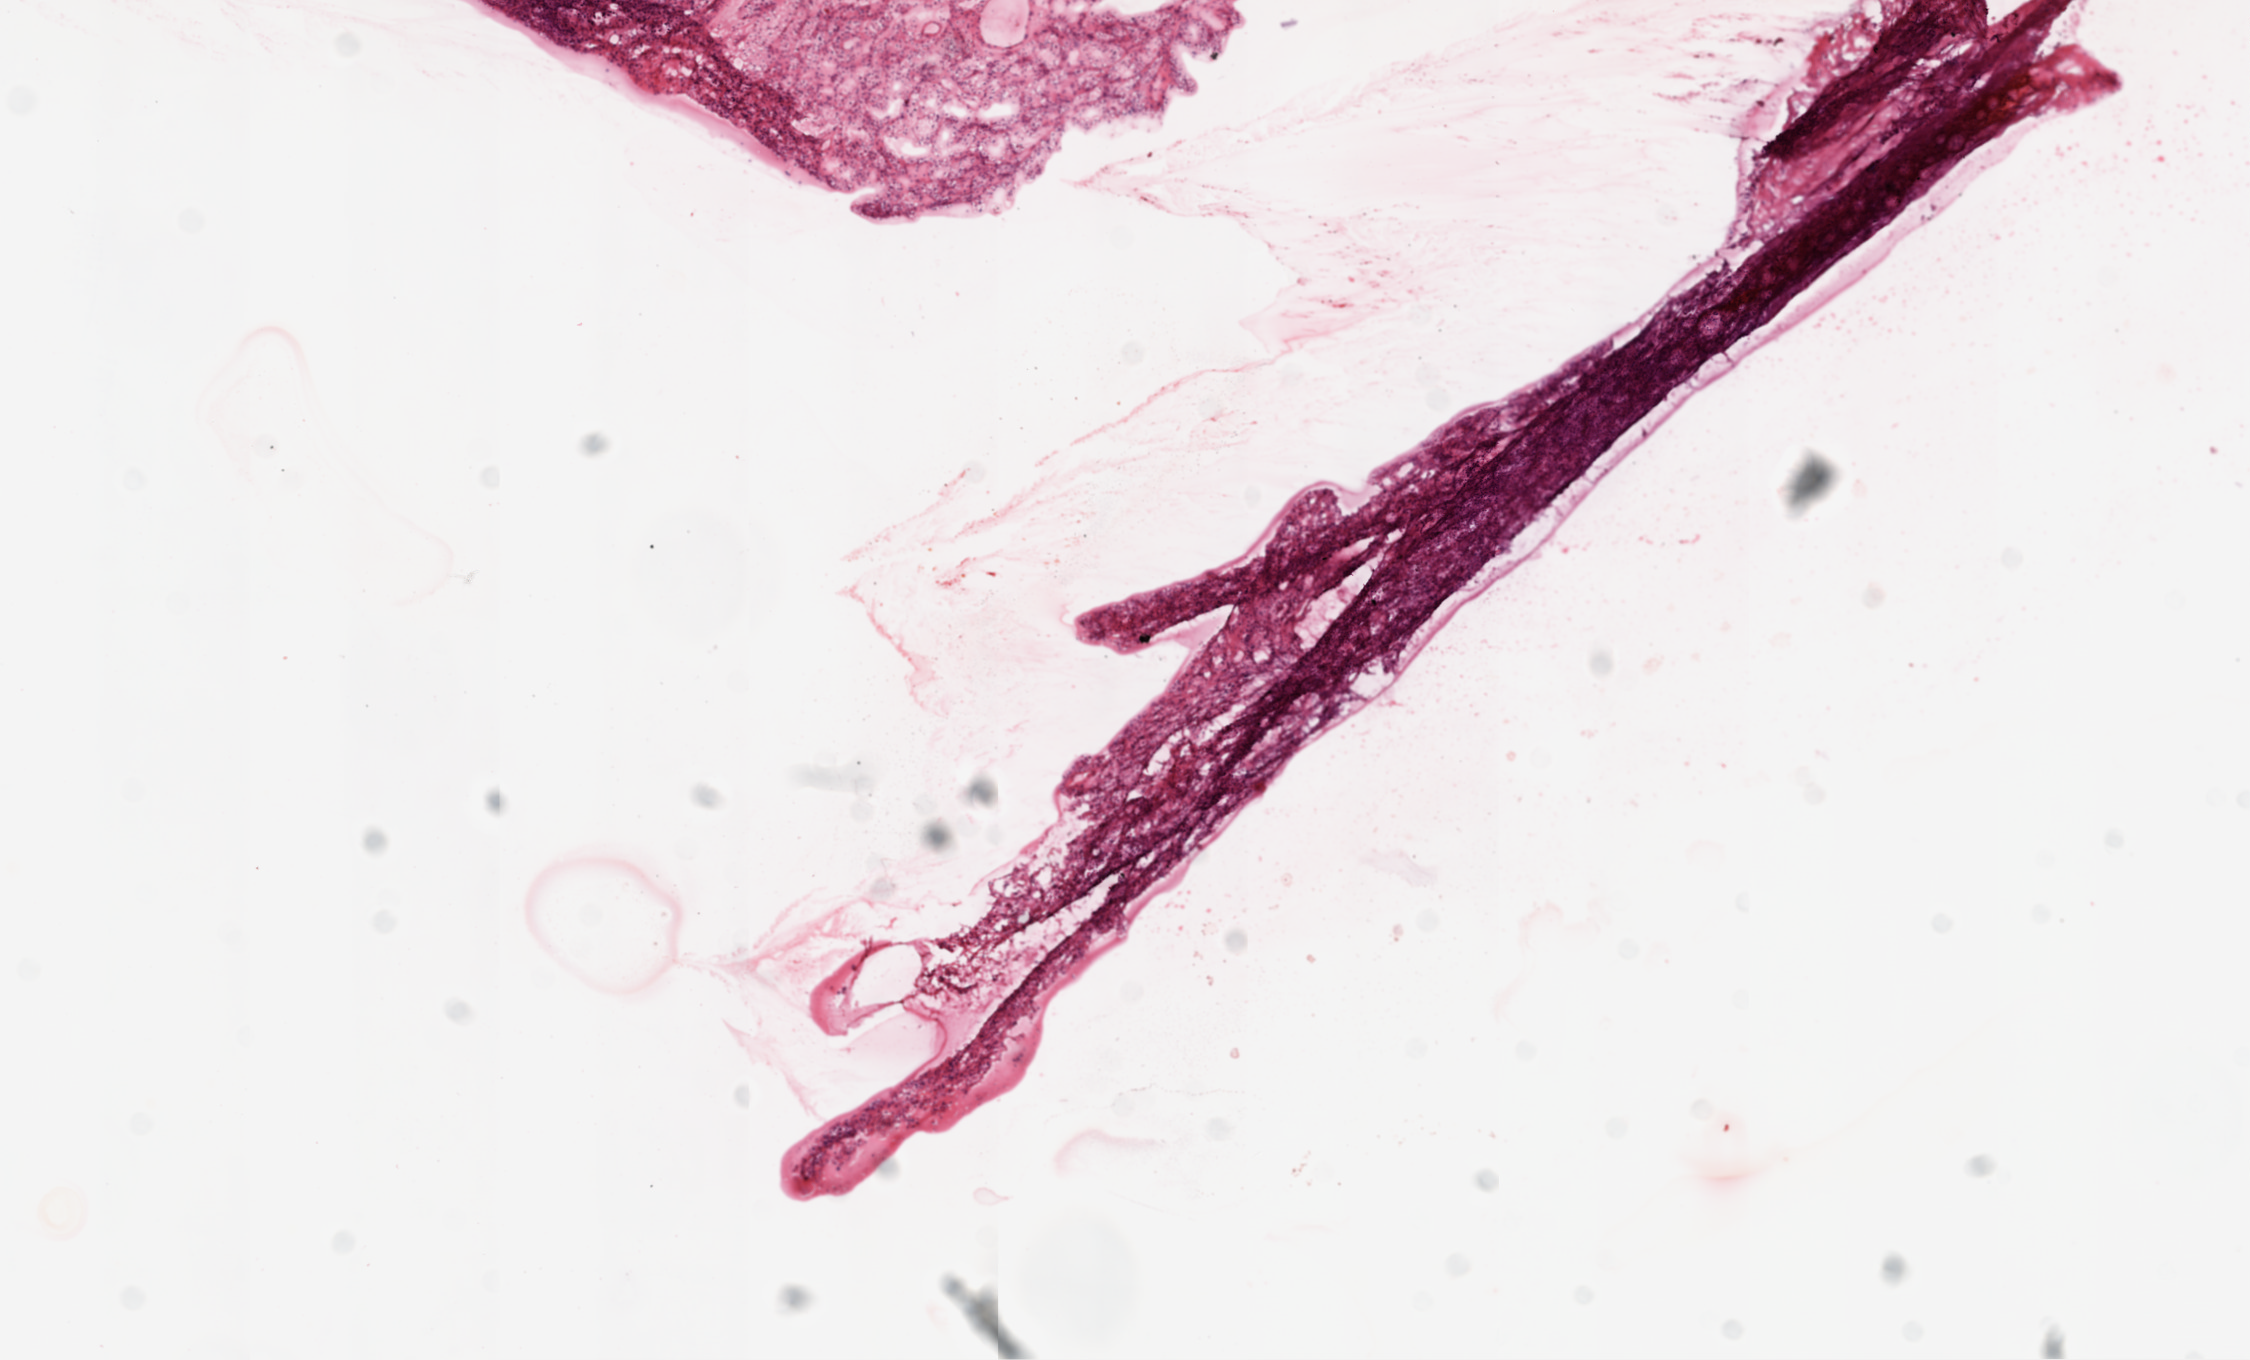
H&E-stained whole-slide image, a low-resolution overview of the entire scanned area, about 9.0 x 5.5 mm (slide scanned at 20x); frozen section; primary tumour sample from the kidney. Male patient; age at initial diagnosis 63 years. Pathologist review of this section (percent, as recorded): tumour cells 90%, tumour nuclei 85%.
Histologic diagnosis: Clear cell adenocarcinoma, NOS.